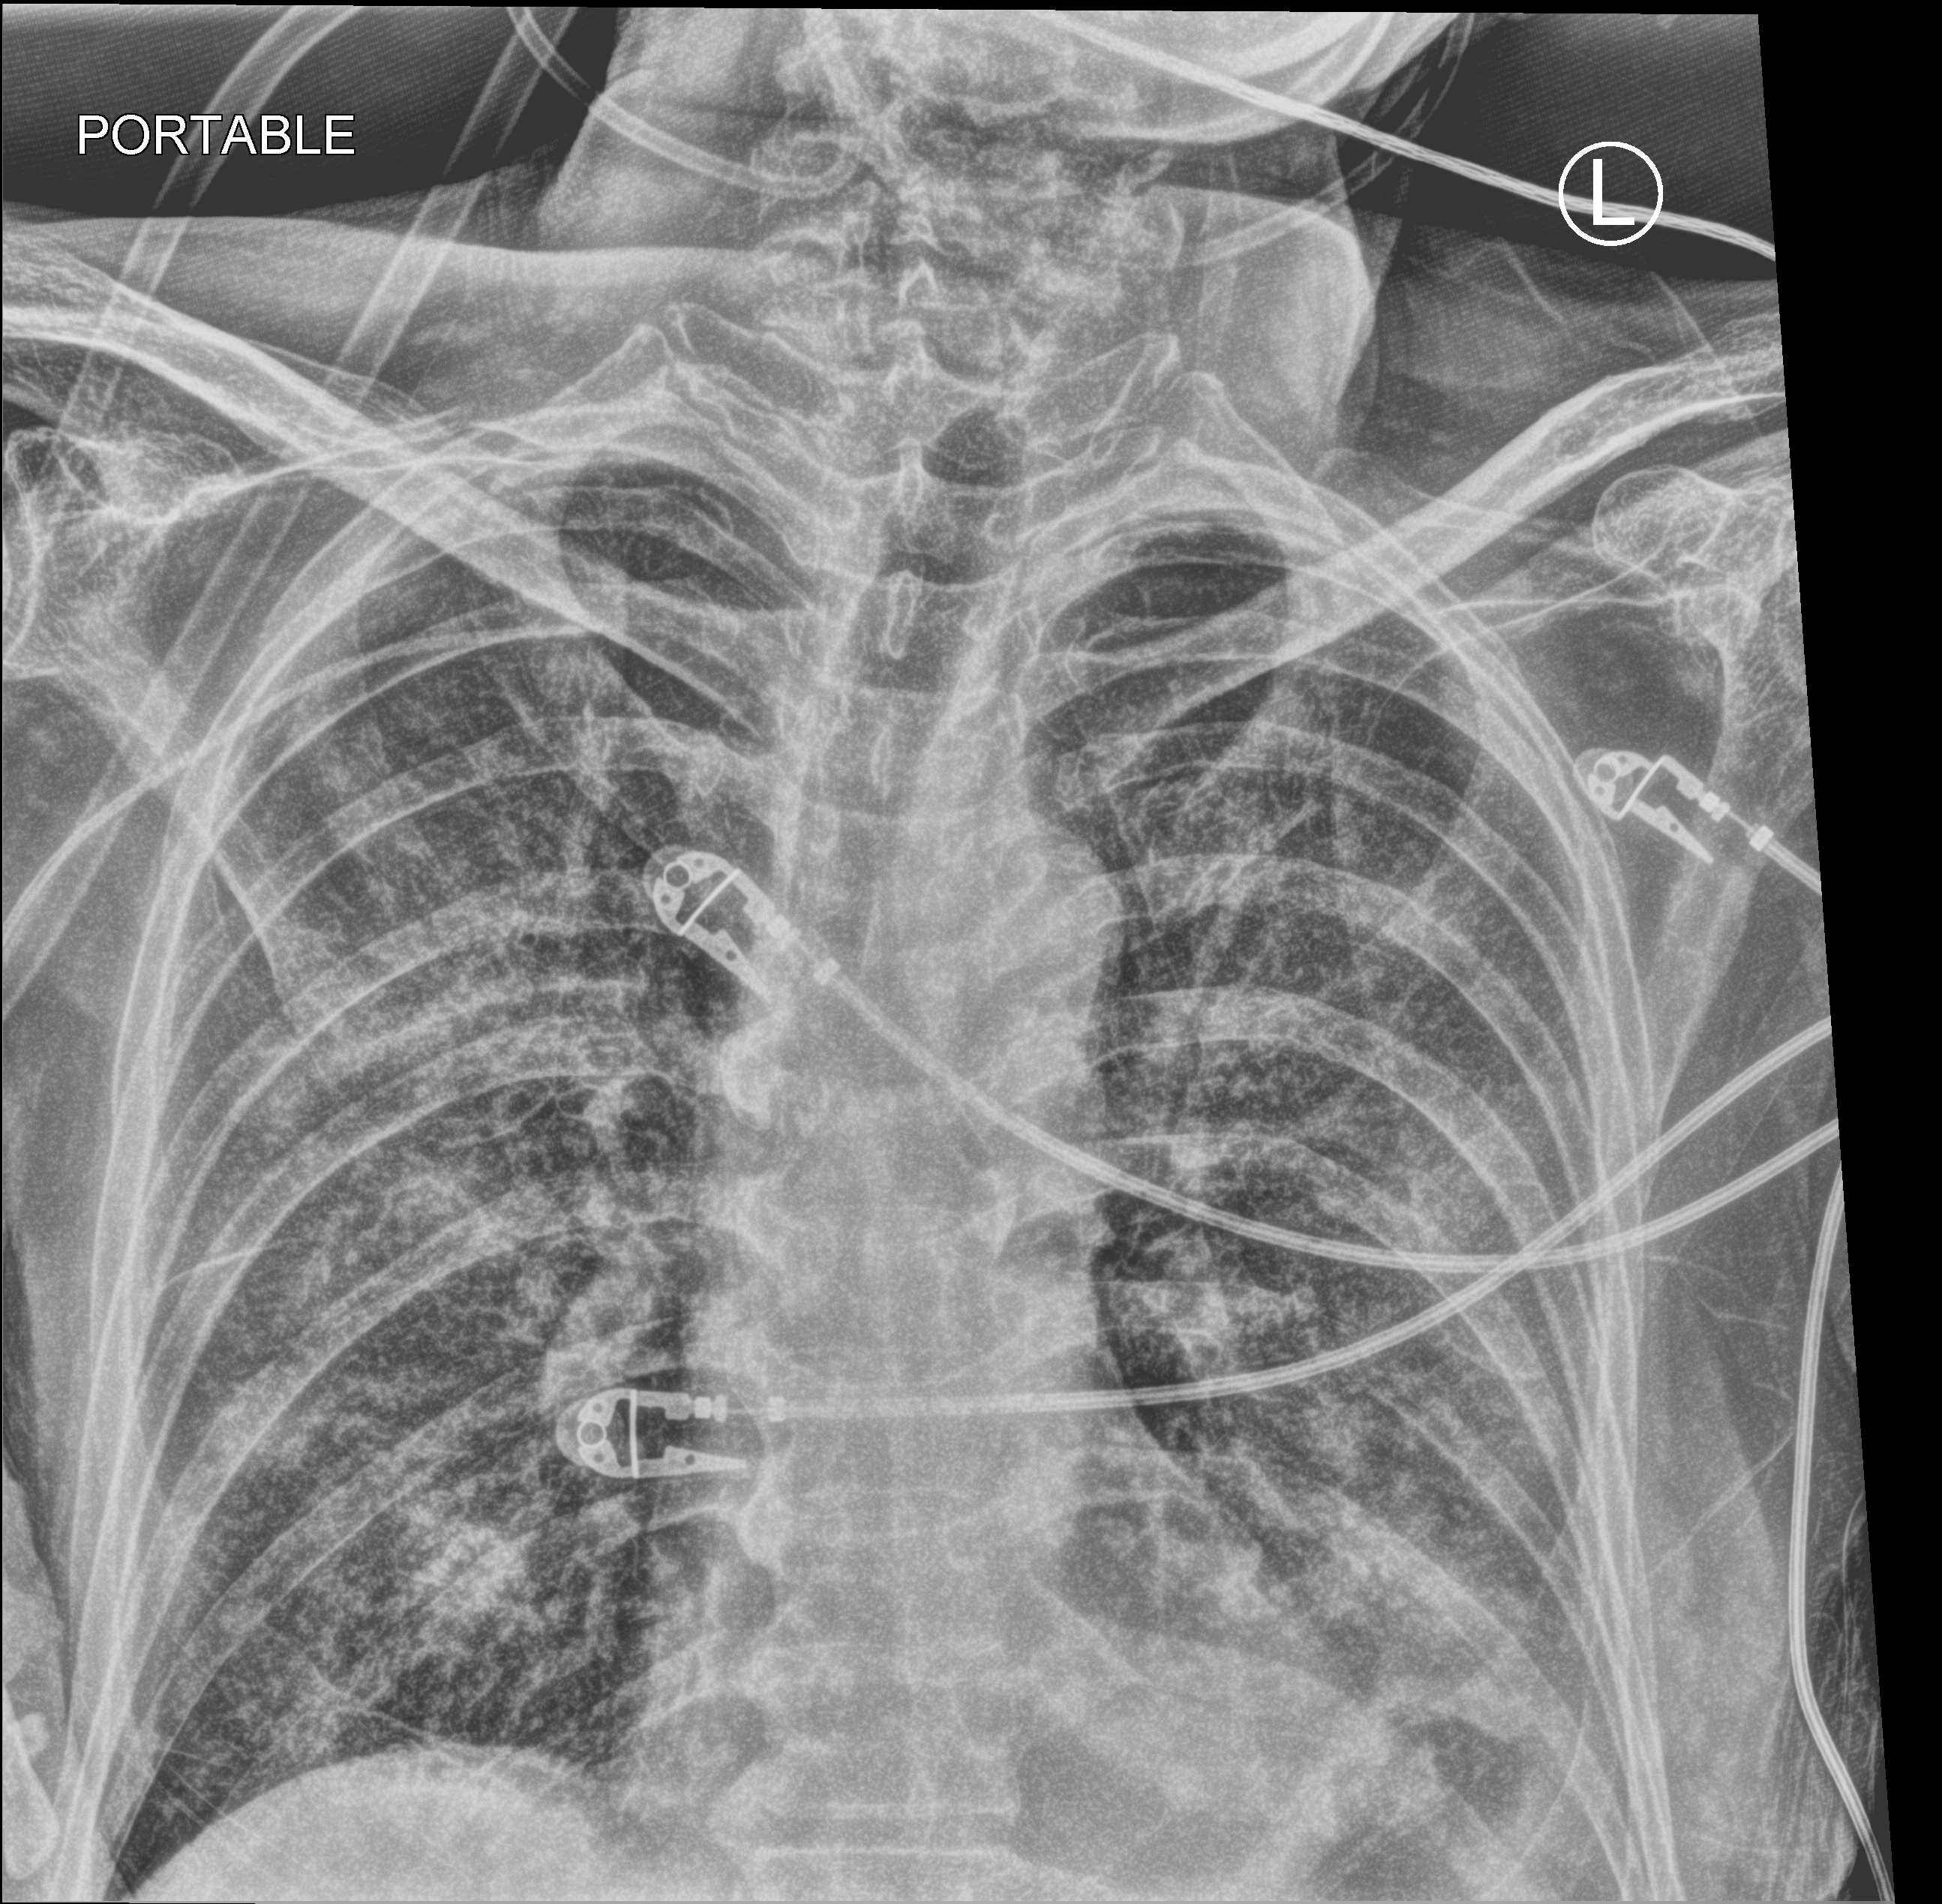
Chest X-ray (portable); anteroposterior (AP) projection. Patient hospitalised with COVID-19; male, aged 60–74 years.
From the hospital-stay record, not from the radiograph (when in the stay this image was taken is not recorded):
- mechanically ventilated during this hospital stay: yes